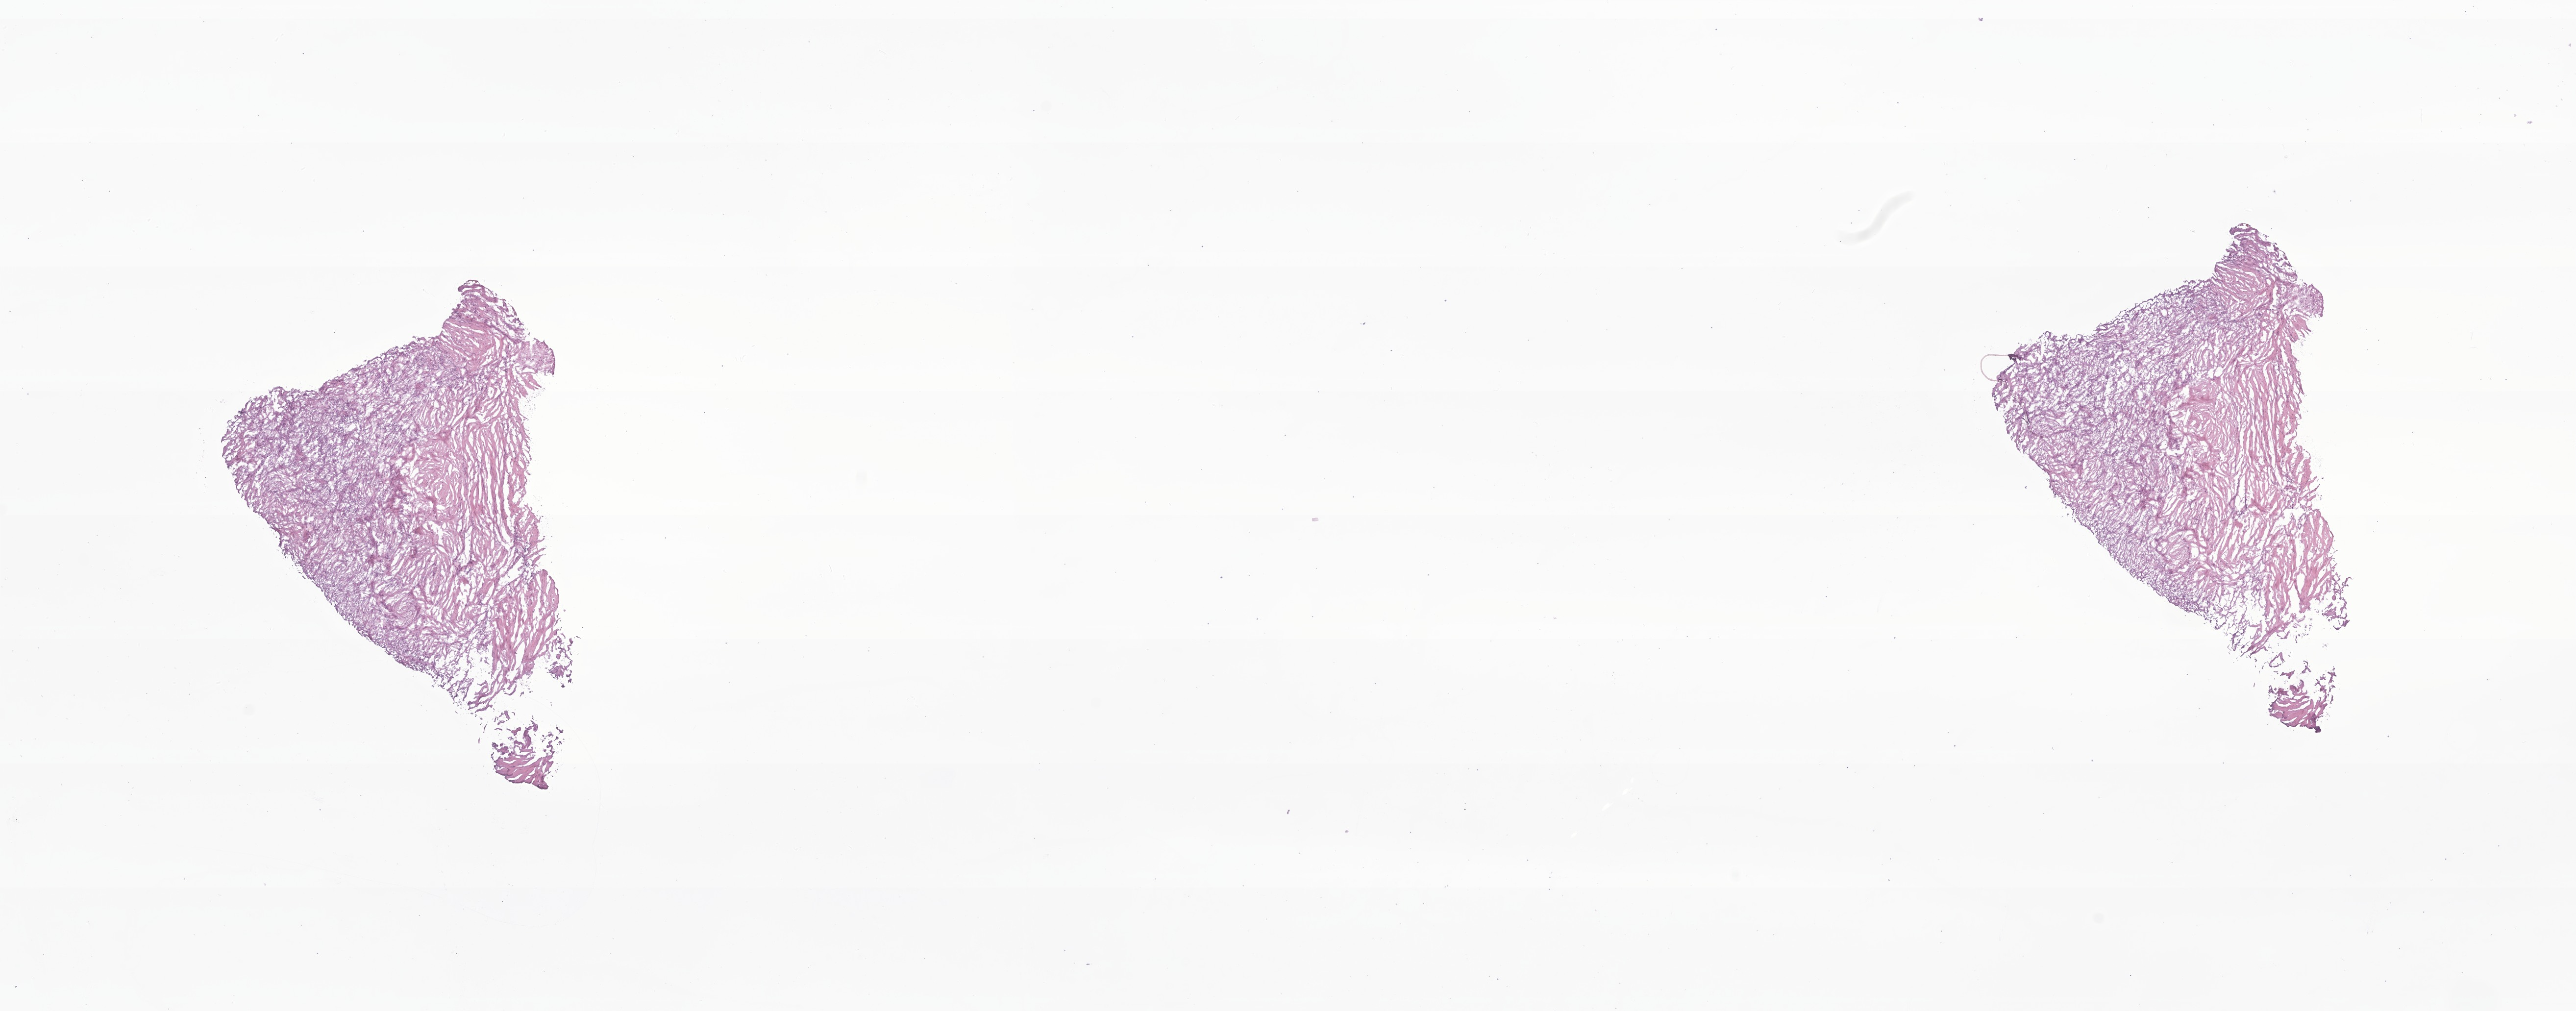
Haematoxylin and eosin whole-slide image of tumor tissue from the meninges, a low-resolution overview of the entire scanned area, about 22.2 x 8.7 mm, frozen section (OCT-embedded). Patient male; age 69 months (5 years 9 months).
Diagnosis (ICD-O-3 morphology term): Meningioma, NOS.